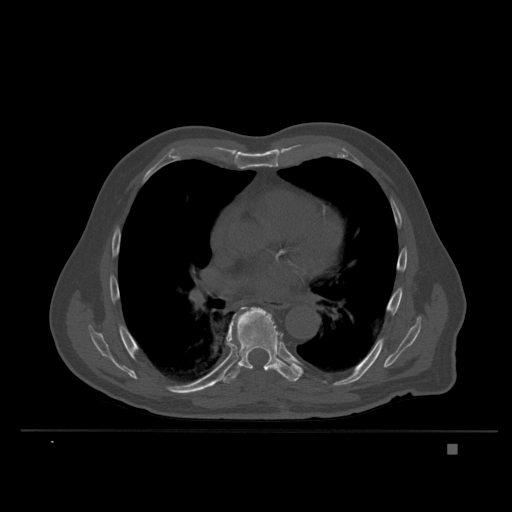
CT including the spine, one axial slice. Slice 235 of 435 in the series (ordered by position). Bone window (W 1800 / L 400 HU). 512 × 512 image matrix, field of view 434 × 434 mm. Male patient, age 73 years. From the clinical record (not read from this slice): primary cancer: skin.
Annotated regions visible in this slice (semi-automatically segmented with operator editing):
- T7 vertebra: bounding box (x1, y1, x2, y2) in pixels: (226, 321, 233, 342)
- T8 vertebra: (220, 307, 301, 384)